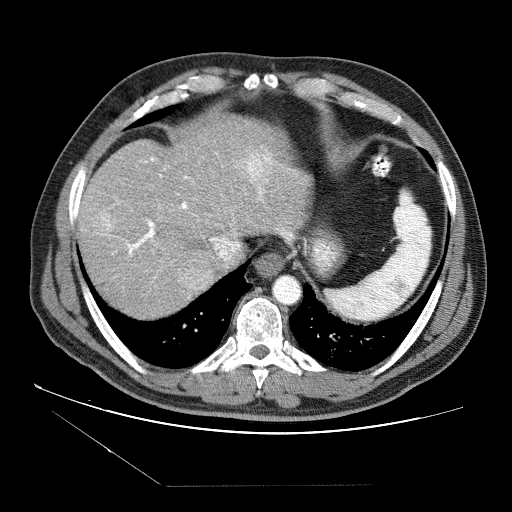
Contrast-enhanced abdominal CT (liver protocol), one axial slice; position 68 of 87 along the scan axis; reconstruction kernel STANDARD; 120 kVp; soft-tissue window (W 400 / L 40 HU); 2.5 mm slice thickness; 512 × 512 image matrix, field of view 400 × 400 mm. Case-level facts recorded for this patient, not image findings: diagnosis: hepatocellular carcinoma (patient treated with transarterial chemoembolisation; whether this scan precedes or follows treatment is not stated here); TNM stage (as recorded): Stage-II; Child-Pugh class: B; tumour differentiation: no biopsy; tumour size: 2.6 cm.
Annotated regions visible in this slice (semi-automatically segmented with operator editing):
- abdominal aorta: bounding box <273,276,300,303> (left, top, right, bottom; pixels)
- liver parenchyma outside the tumour (the mass and vessels are separate outlines, so this box may not span the whole liver): <78,116,312,318>
- mass: <92,145,273,291>
- liver vessels: <82,153,292,278>